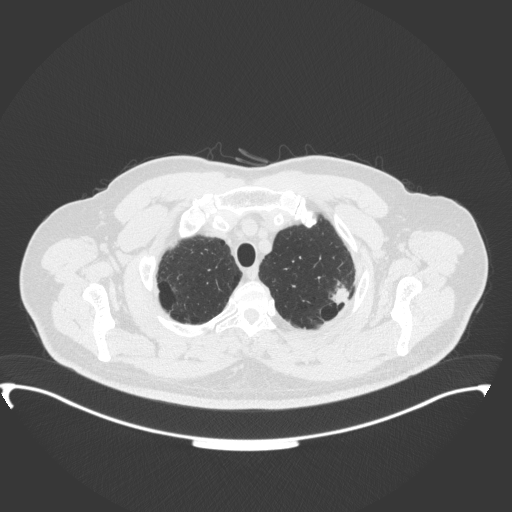
Chest CT, one axial slice. Slice 318 of 350 in the series (ordered by position). 120 kVp. Lung window (W 1500 / L -600 HU). 1 mm slice thickness. 512 × 512 image matrix, field of view 459 × 459 mm. Patient: male, 64 years. Case-level facts recorded for this patient, not image findings: clinical TNM (as recorded): T1c N1 M1.
Structures marked on this image (rectangle marked by the reading radiologist):
- lung tumour (recorded histology: adenocarcinoma): bounding box [x1, y1, x2, y2] px = [326, 280, 353, 308]